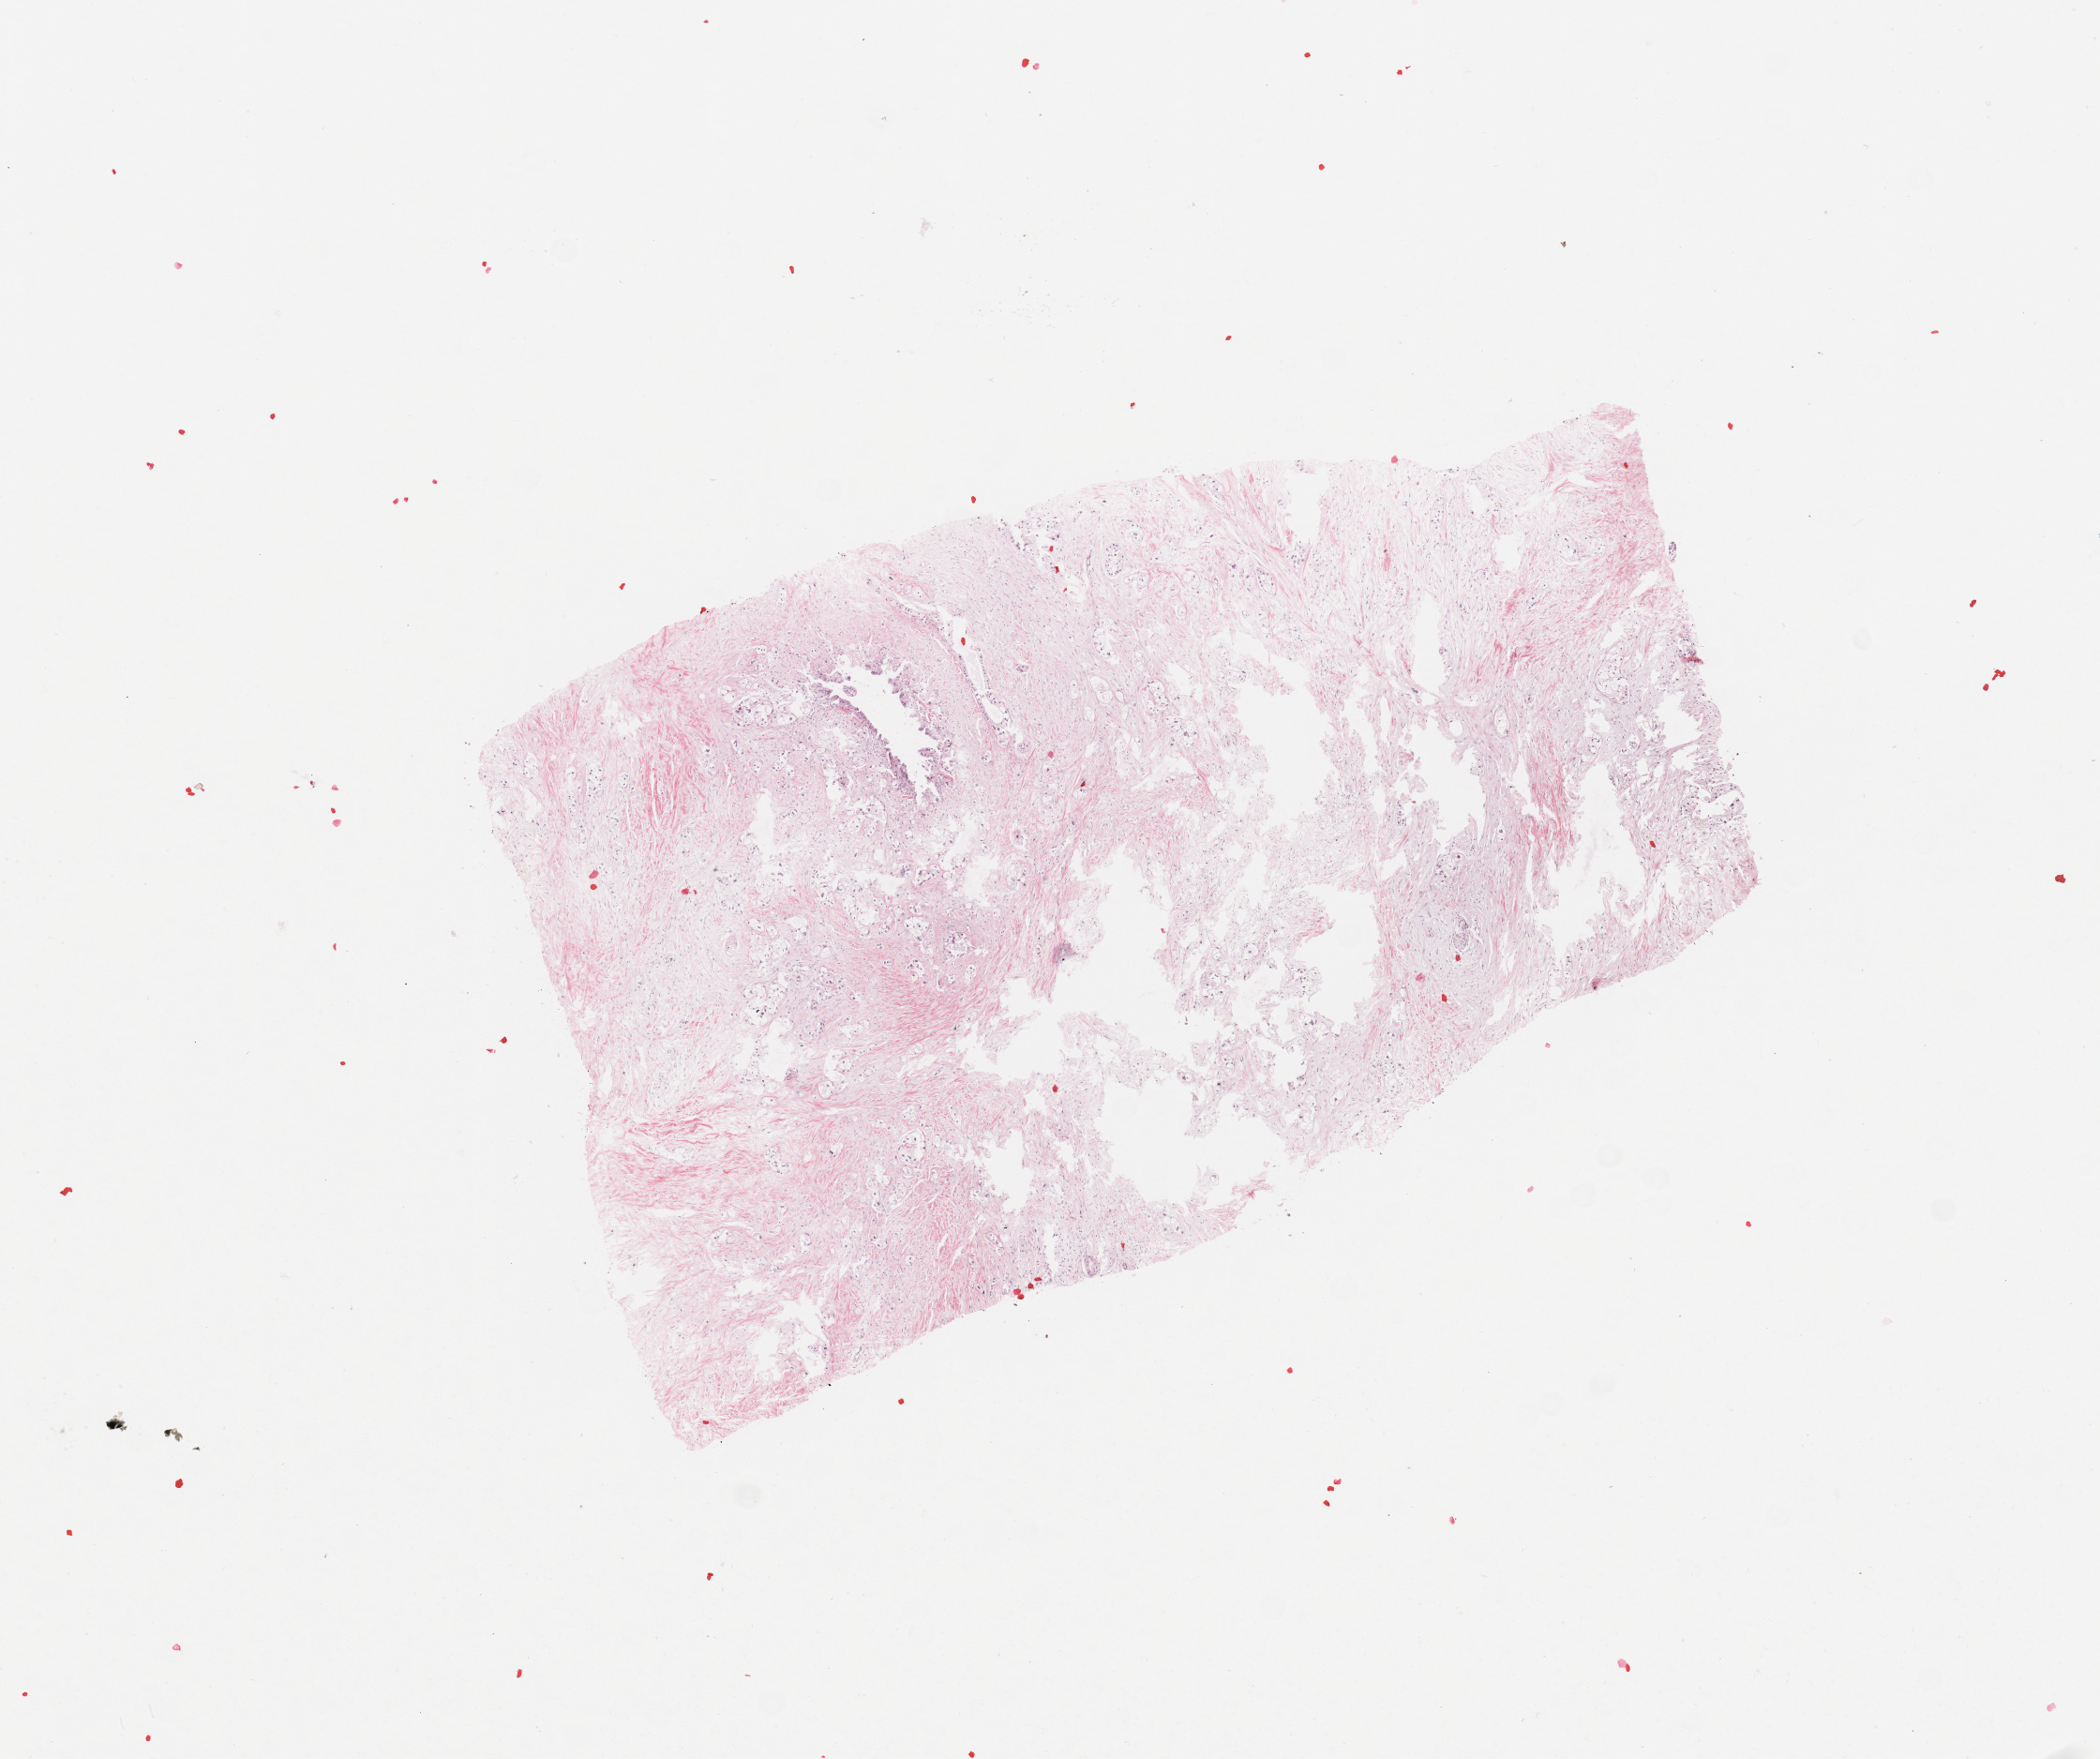
Whole-slide histology image, H&E-stained, shown as a low-resolution overview of the whole scanned area (about 8.9 x 7.4 mm); pancreas, tissue type not recorded.
- patient diagnosis (cohort enrolment): ductal adenocarcinoma (pancreas)